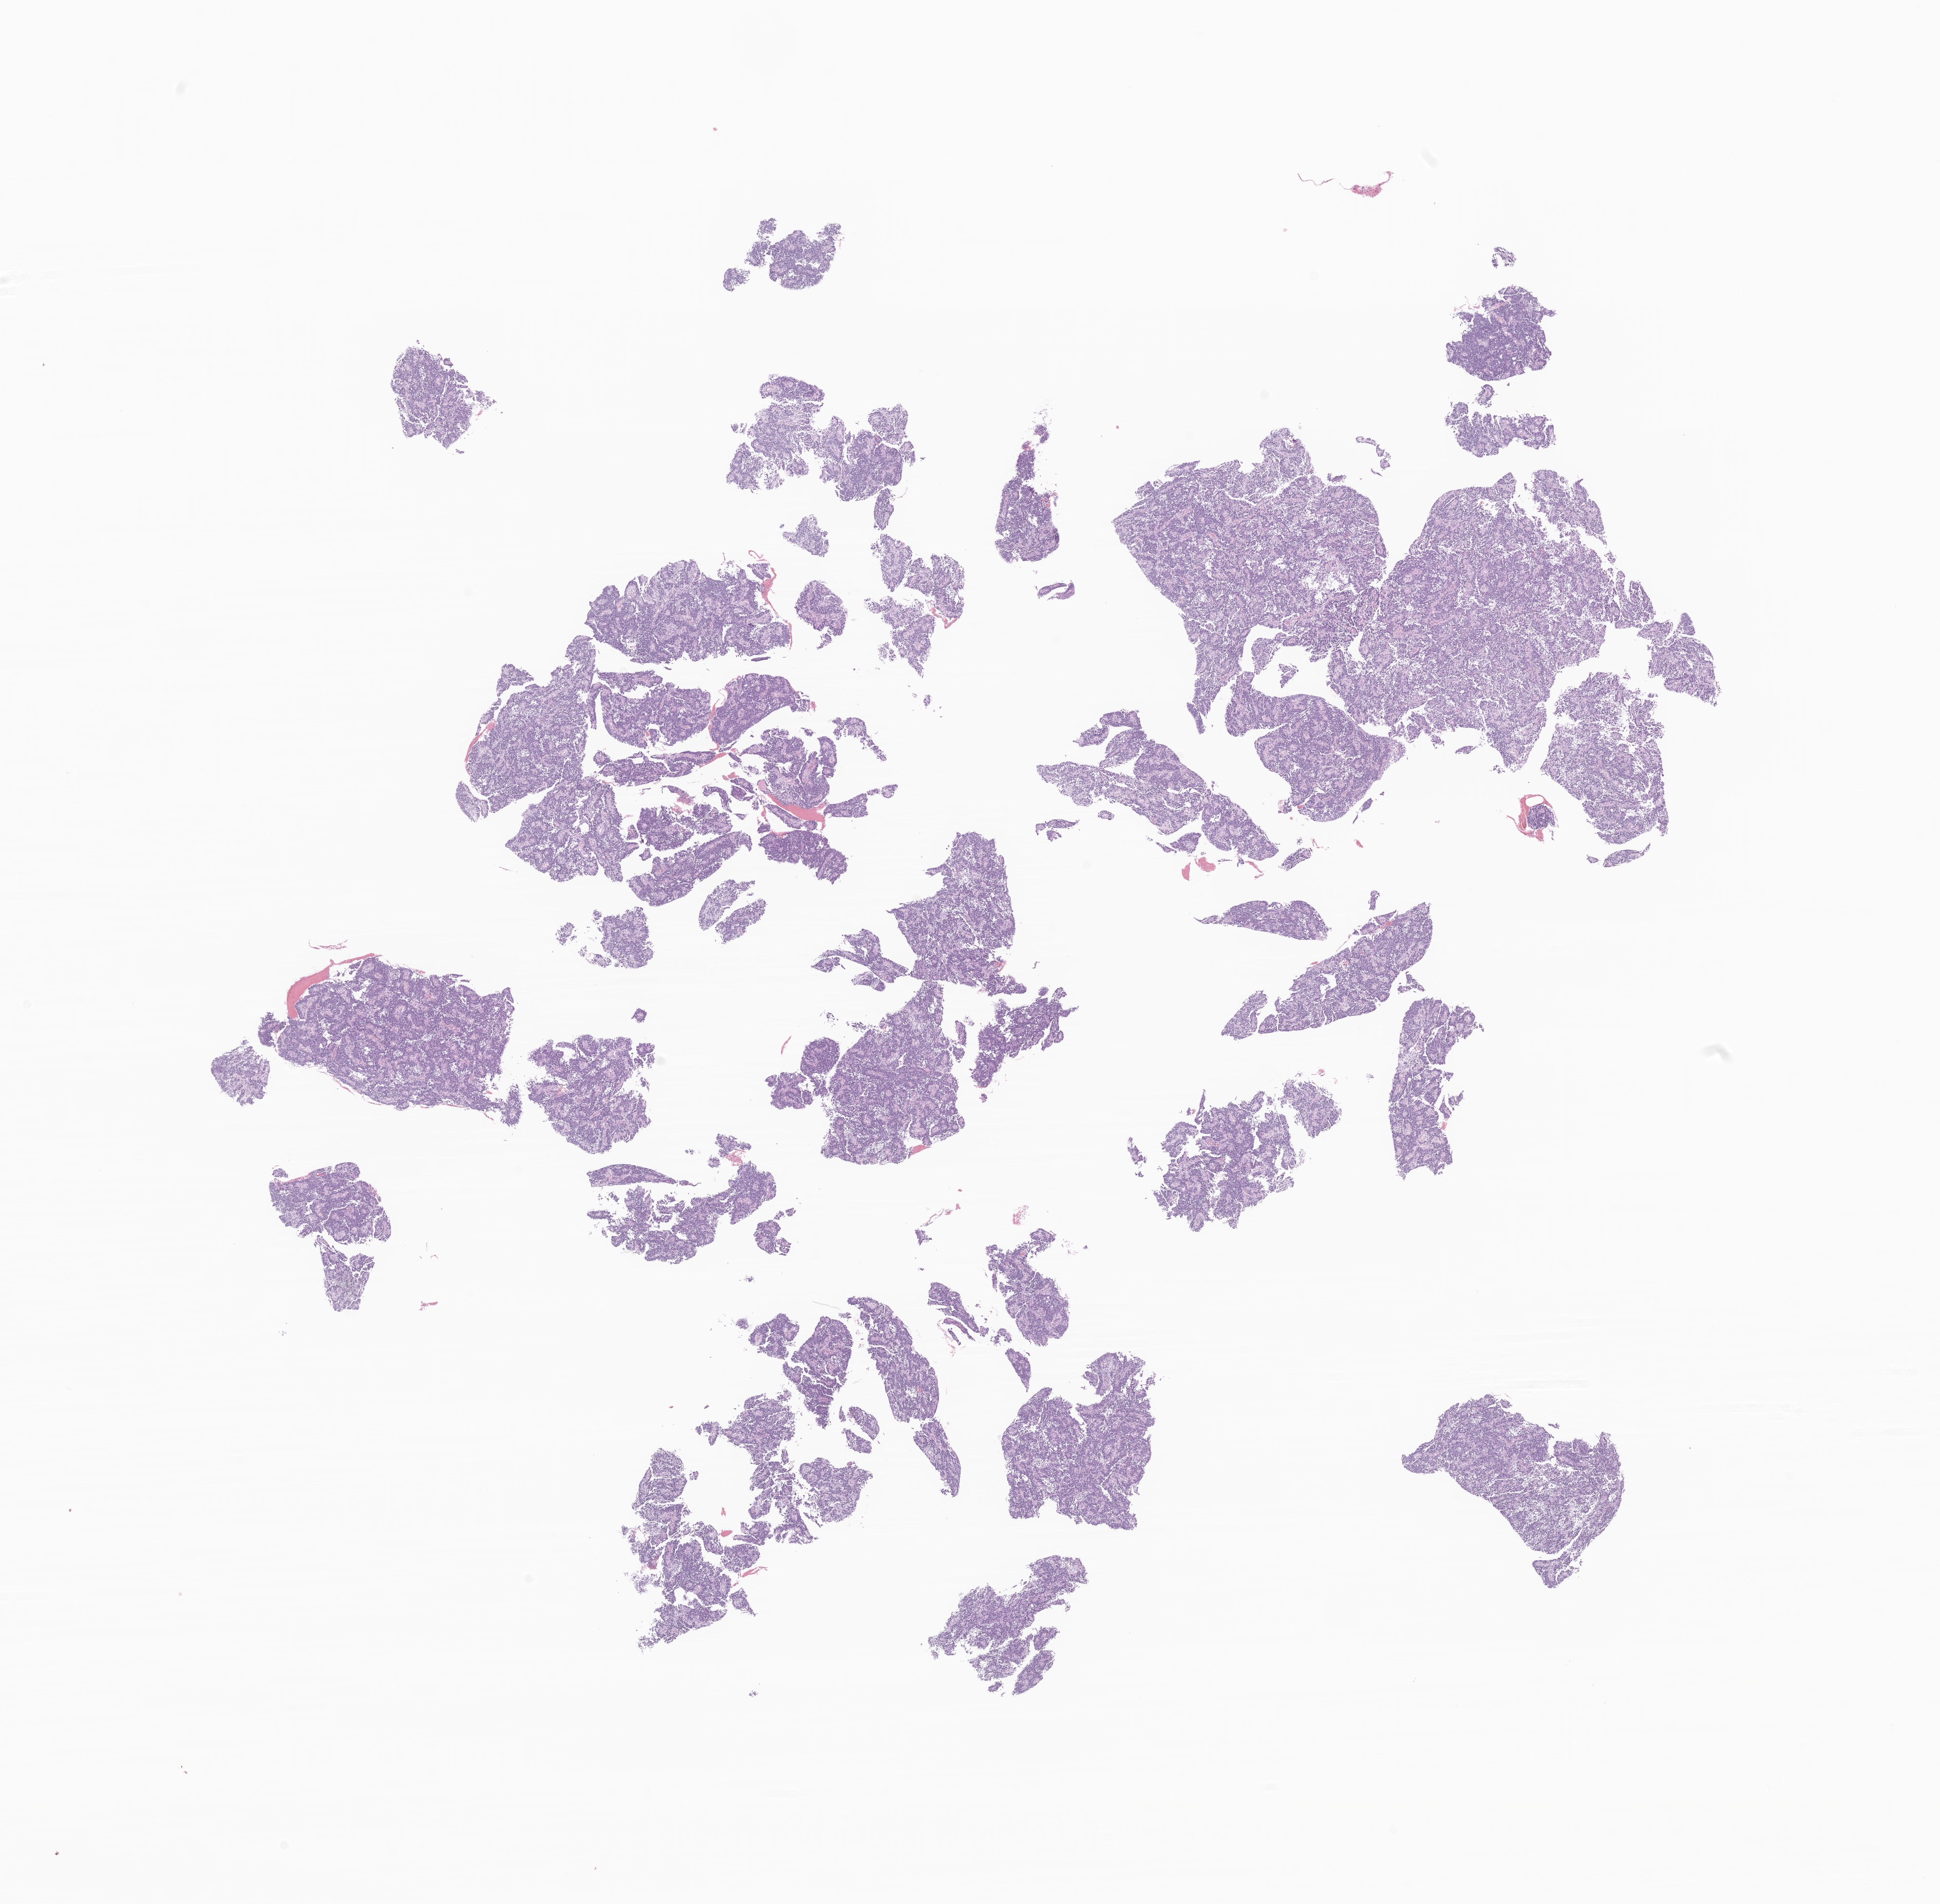
Whole-slide image, haematoxylin and eosin stain of tumor tissue from the brain, a low-resolution overview of the entire scanned area, about 16.8 x 16.5 mm; formalin-fixed, paraffin-embedded (FFPE) tissue. Female patient, age 93 months (7 years 9 months).
Diagnosis (ICD-O-3 morphology term): Neoplasm, malignant.